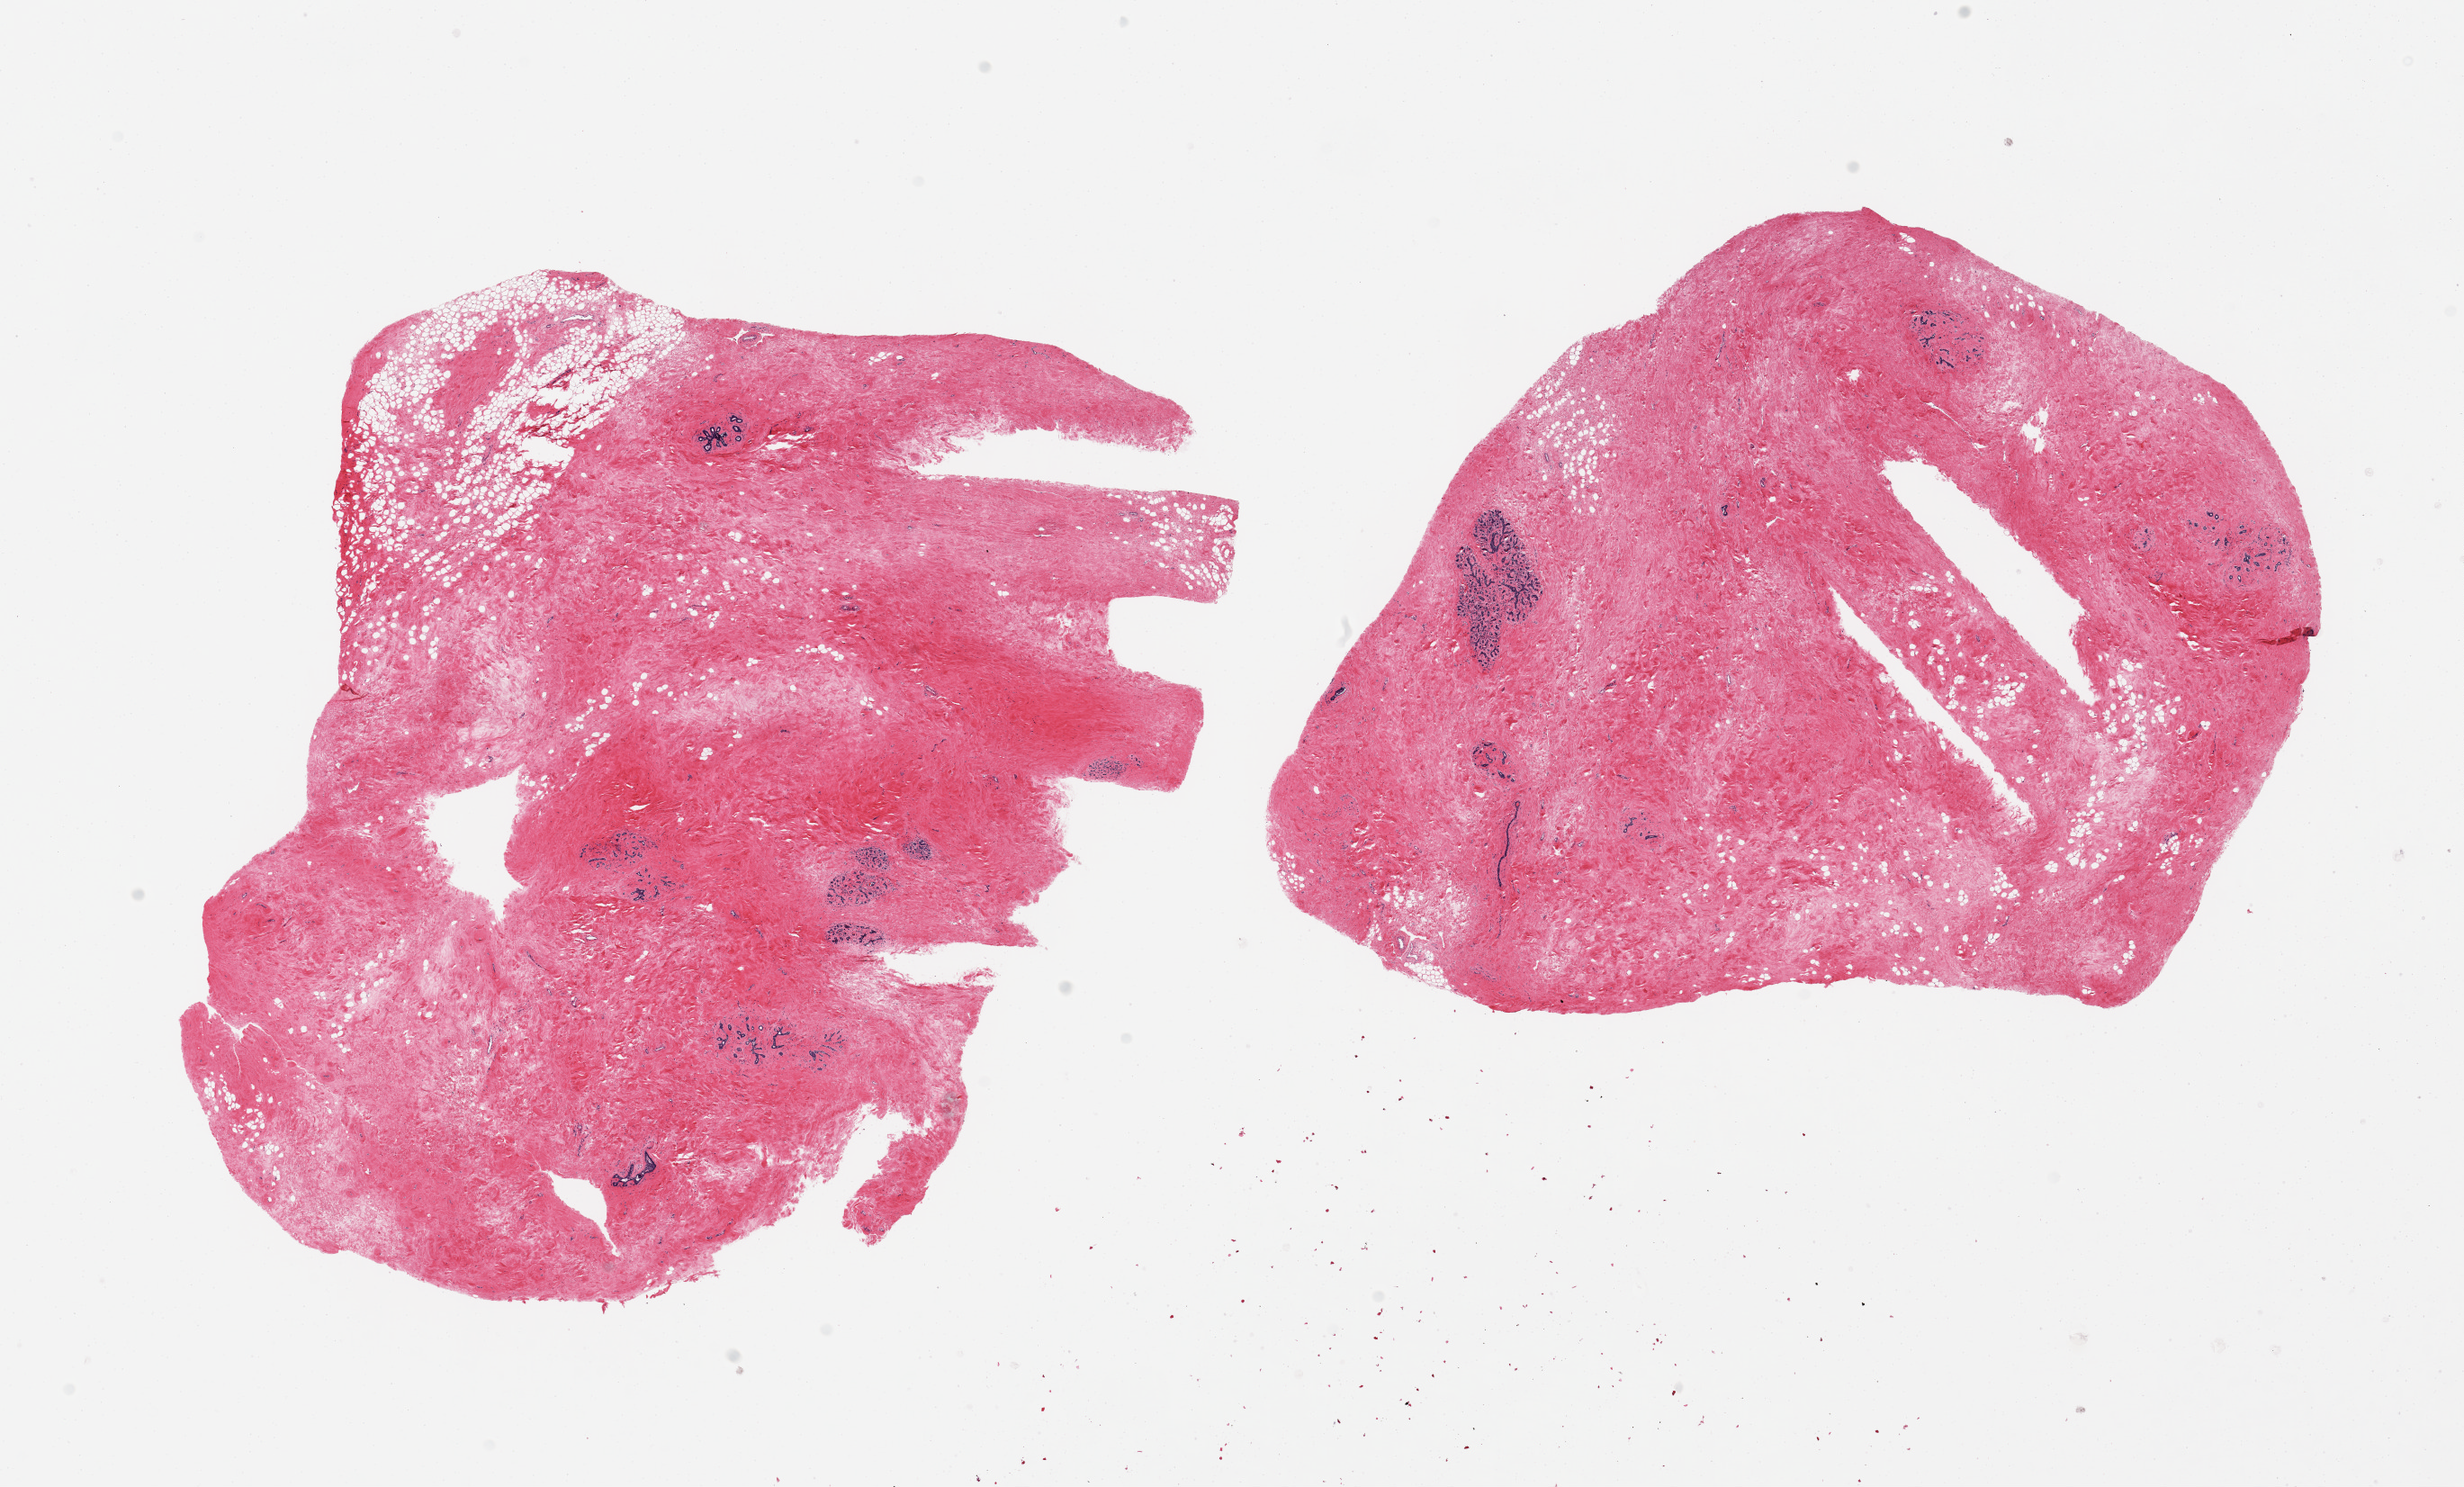
Whole-slide image, hematoxylin and eosin (H&E) stain, brightfield, low-resolution overview of the scanned area, about 21.7 x 13.1 mm; PAXgene-fixed, paraffin-embedded tissue; target tissue: breast; donor tissue sample.
* reviewer comment on this tissue sample: 2 piecesm inactive lobular units; prominent stromal fibrosis